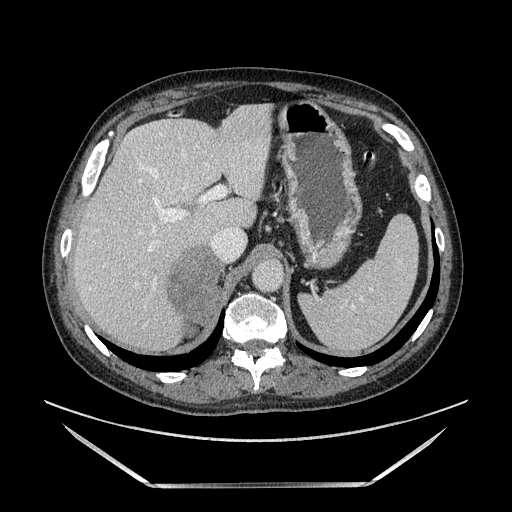
Contrast-enhanced abdominal CT, one axial slice. Position 106 of 185 along the scan axis. Soft-tissue window (W 400 / L 40 HU). 1.25 mm slice thickness. 512 × 512 image matrix, field of view 440 × 440 mm. Male patient. Case-level facts recorded for this patient, not image findings: diagnosis: adrenocortical carcinoma; tumour side: right adrenal; tumour size at pathology: 10.3 cm; Ki-67 index: 20 %; stage (as recorded): 3.
Structures marked on this image (semi-automatically segmented with operator editing):
- mass: bounding box (x1, y1, x2, y2) in pixels: (171, 246, 223, 331)